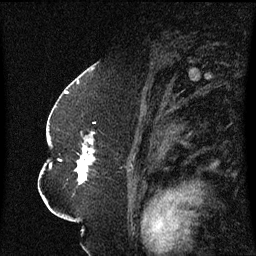
Breast MRI (dynamic contrast-enhanced), one sagittal slice; dynamic contrast-enhanced series, image 2 of 3 at this slice position (ordered by acquisition); 1.5 T; TE 4.2 ms, TR 8.4 ms; 2.3 mm slice thickness; 256 × 256 image matrix, field of view 200 × 200 mm. Female patient, age 52 years. From the clinical record (not read from this slice): setting: breast cancer imaged before/during neoadjuvant chemotherapy; receptor status: HR-positive, HER2-negative.
Outlined on this slice (semi-automatically segmented with operator editing):
- analysis volume of interest (the breast-tissue region the enhancement analysis was run in; not a lesion): bounding box (x1, y1, x2, y2) in pixels: (49, 124, 122, 197)
- tumour enhancement mask (voxels above the 70 % enhancement threshold inside the analysis volume of interest): (76, 132, 94, 185)